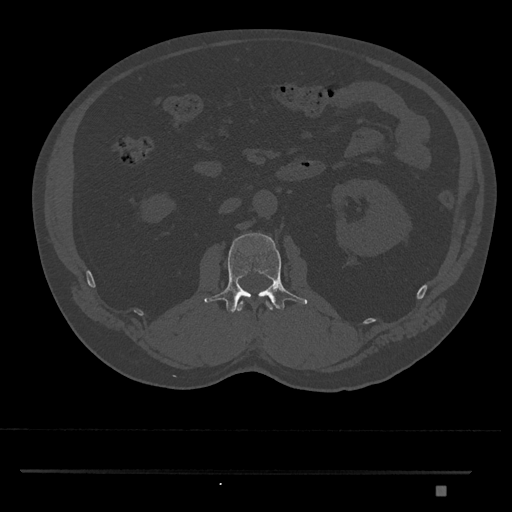
CT including the spine, one axial slice; position 762 of 1134 along the scan axis; reconstruction kernel Br40s/3; bone window (W 1800 / L 400 HU); 0.5 mm slice thickness; 512 × 512 image matrix, field of view 429 × 429 mm. Patient: male, 65 years. Case-level facts recorded for this patient, not image findings: primary cancer: prostate.
Annotated regions visible in this slice (semi-automatic segmentation, software-assisted and operator-edited):
- L1 vertebra: bounding box <236,301,273,312> (left, top, right, bottom; pixels)
- L2 vertebra: <204,233,308,313>